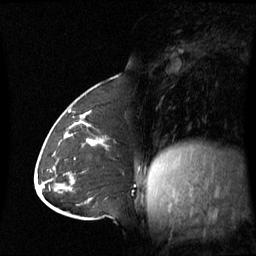
Breast MRI (dynamic contrast-enhanced), one sagittal slice; position 26 of 60 along the scan axis; dynamic contrast-enhanced series, image 2 of 3 at this slice position (ordered by acquisition); 1.5 T; TE 4.2 ms, TR 8.4 ms; 2.8 mm slice thickness; 256 × 256 image matrix, field of view 270 × 270 mm. Patient: female, 43 years. From the clinical record (not read from this slice): setting: breast cancer imaged before/during neoadjuvant chemotherapy; receptor status: triple-negative.
Annotated regions visible in this slice (semi-automatically segmented with operator editing):
- analysis volume of interest (the breast-tissue region the enhancement analysis was run in; not a lesion): bounding box [x1, y1, x2, y2] px = [62, 124, 137, 180]
- tumour enhancement mask (voxels above the 70 % enhancement threshold inside the analysis volume of interest): [73, 124, 99, 146]